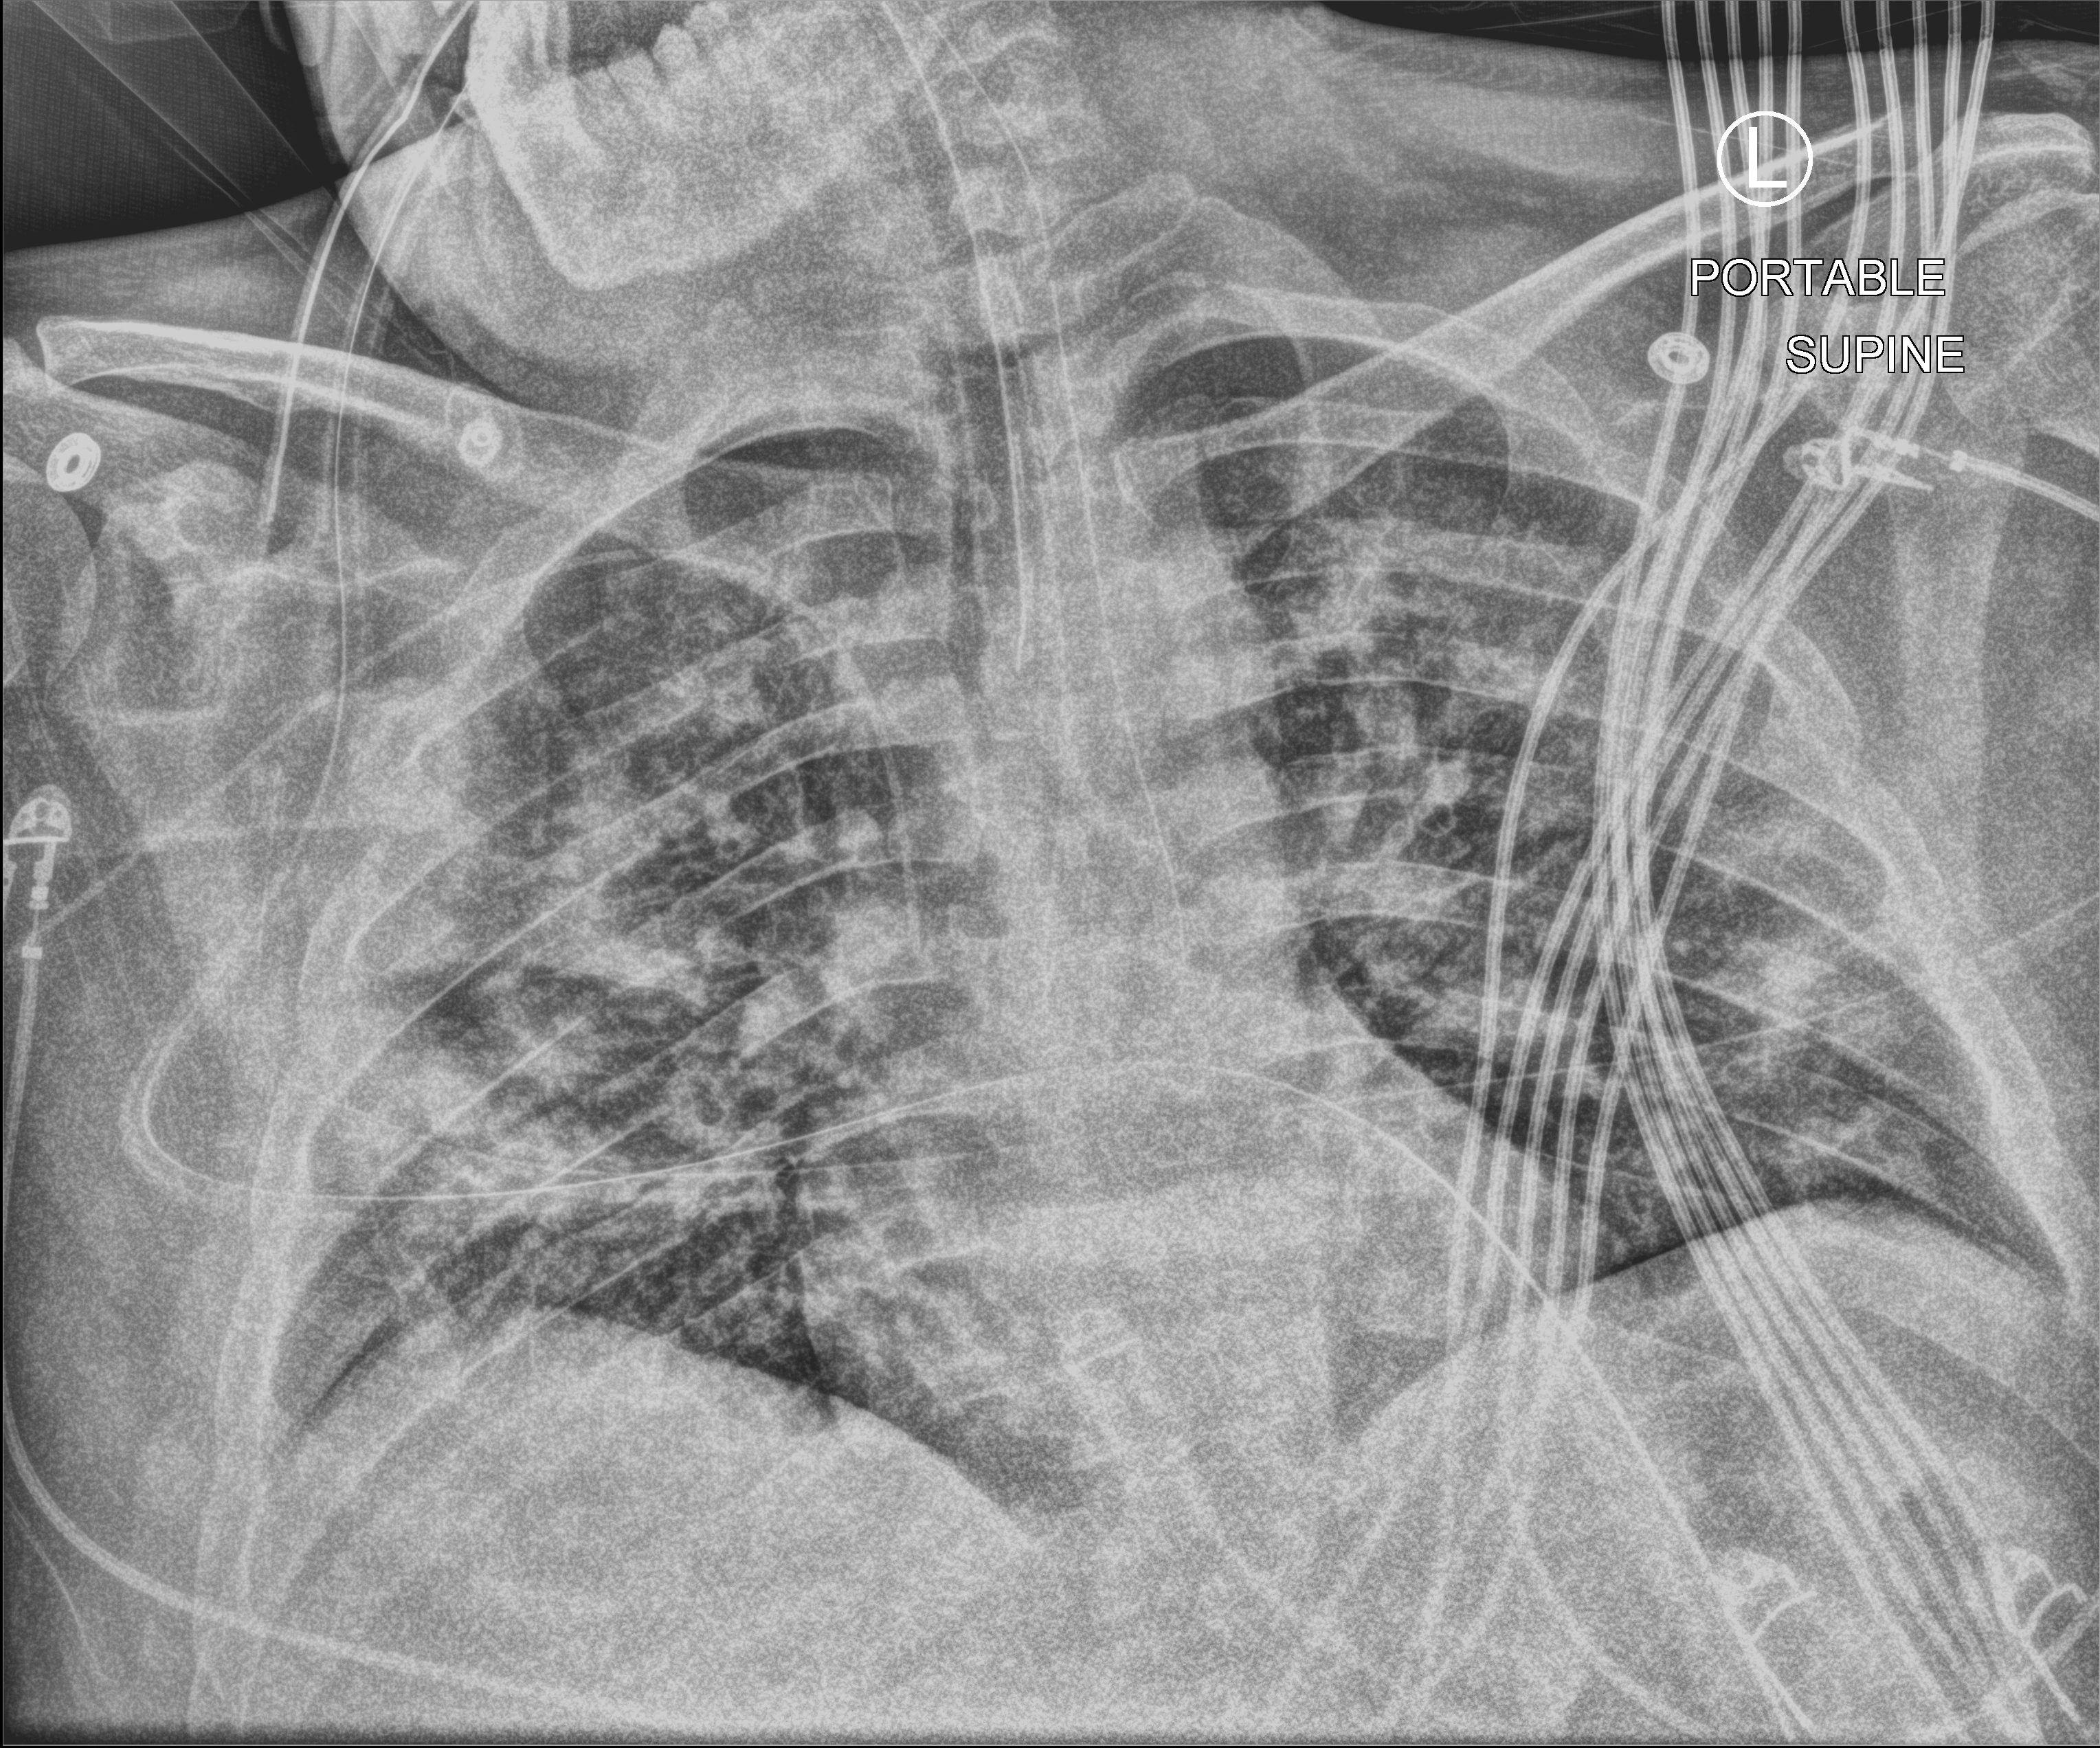
Portable chest radiograph. Patient hospitalised with COVID-19; female, aged 18–59 years.
From the hospital-stay record, not from the radiograph (when in the stay this image was taken is not recorded): admitted to intensive care during this hospital stay: yes.